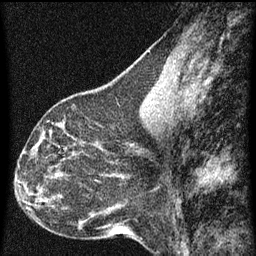
Breast MRI (dynamic contrast-enhanced), one sagittal slice; dynamic contrast-enhanced series, image 2 of 3 at this slice position (ordered by acquisition); 1.5 T; TE 4.2 ms, TR 8 ms; 2 mm slice thickness; 256 × 256 image matrix, field of view 180 × 180 mm. Female patient, age 44 years.
Outlined on this slice (semi-automatic segmentation, software-assisted and operator-edited):
- analysis volume of interest (the breast-tissue region the enhancement analysis was run in; not a lesion): bounding box [x1, y1, x2, y2] px = [49, 128, 95, 169]
- tumour enhancement mask (voxels above the 70 % enhancement threshold inside the analysis volume of interest): [50, 130, 83, 169]